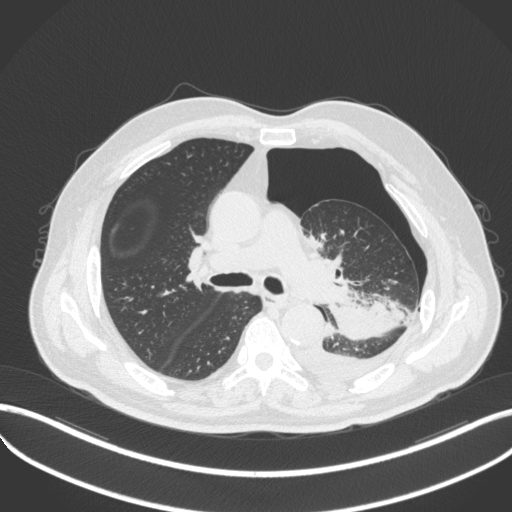
Chest CT, one axial slice. 120 kVp. Lung window (W 1500 / L -600 HU). 1 mm slice thickness. 512 × 512 image matrix, field of view 400 × 400 mm. Patient: male, 76 years. From the clinical record (not read from this slice): clinical TNM (as recorded): T3 N0 M1b.
Structures marked on this image (bounding box drawn by a radiologist):
- lung tumour (recorded histology: adenocarcinoma): box from (x=326, y=283) to (x=408, y=346) px